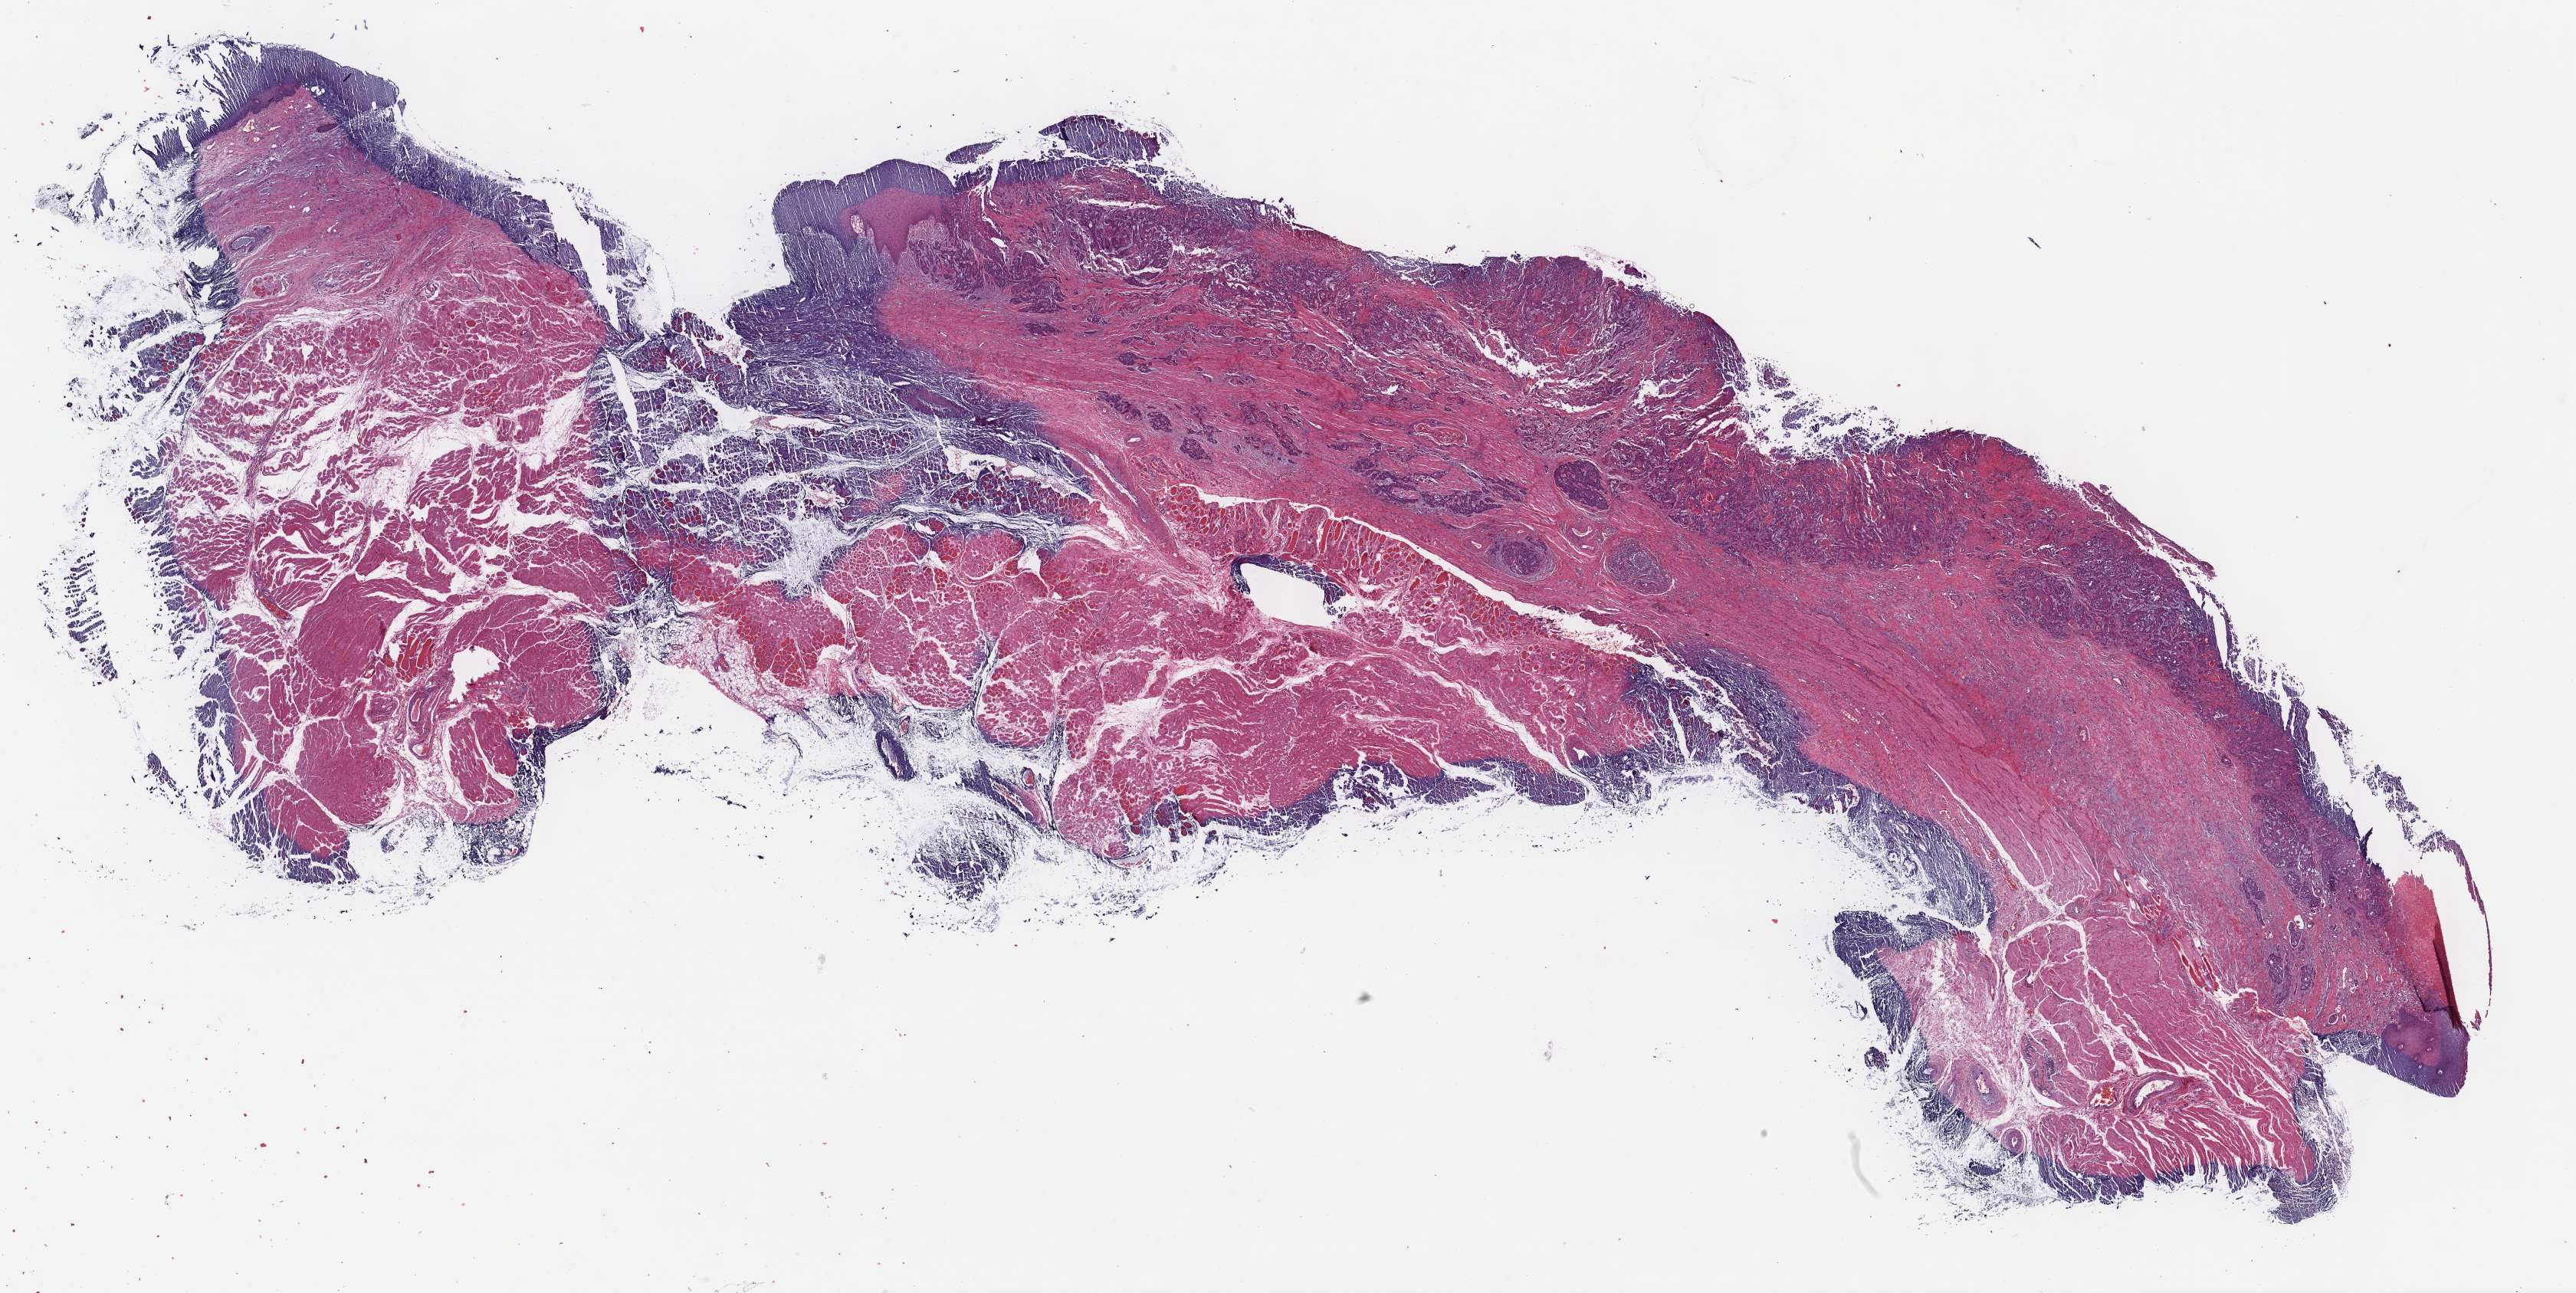
Hematoxylin and eosin (H&E) stained whole-slide image — a low-resolution overview of the entire scanned area, about 27.2 x 13.6 mm (acquisition: 40x scan), FFPE section, head and neck, primary tumour sample. Male patient; age at initial diagnosis 55 years. Histologic grade: G2 (moderately differentiated).
* AJCC pathologic stage: III (7th edition)
* pathologic diagnosis: Squamous cell carcinoma, NOS (larynx, NOS)